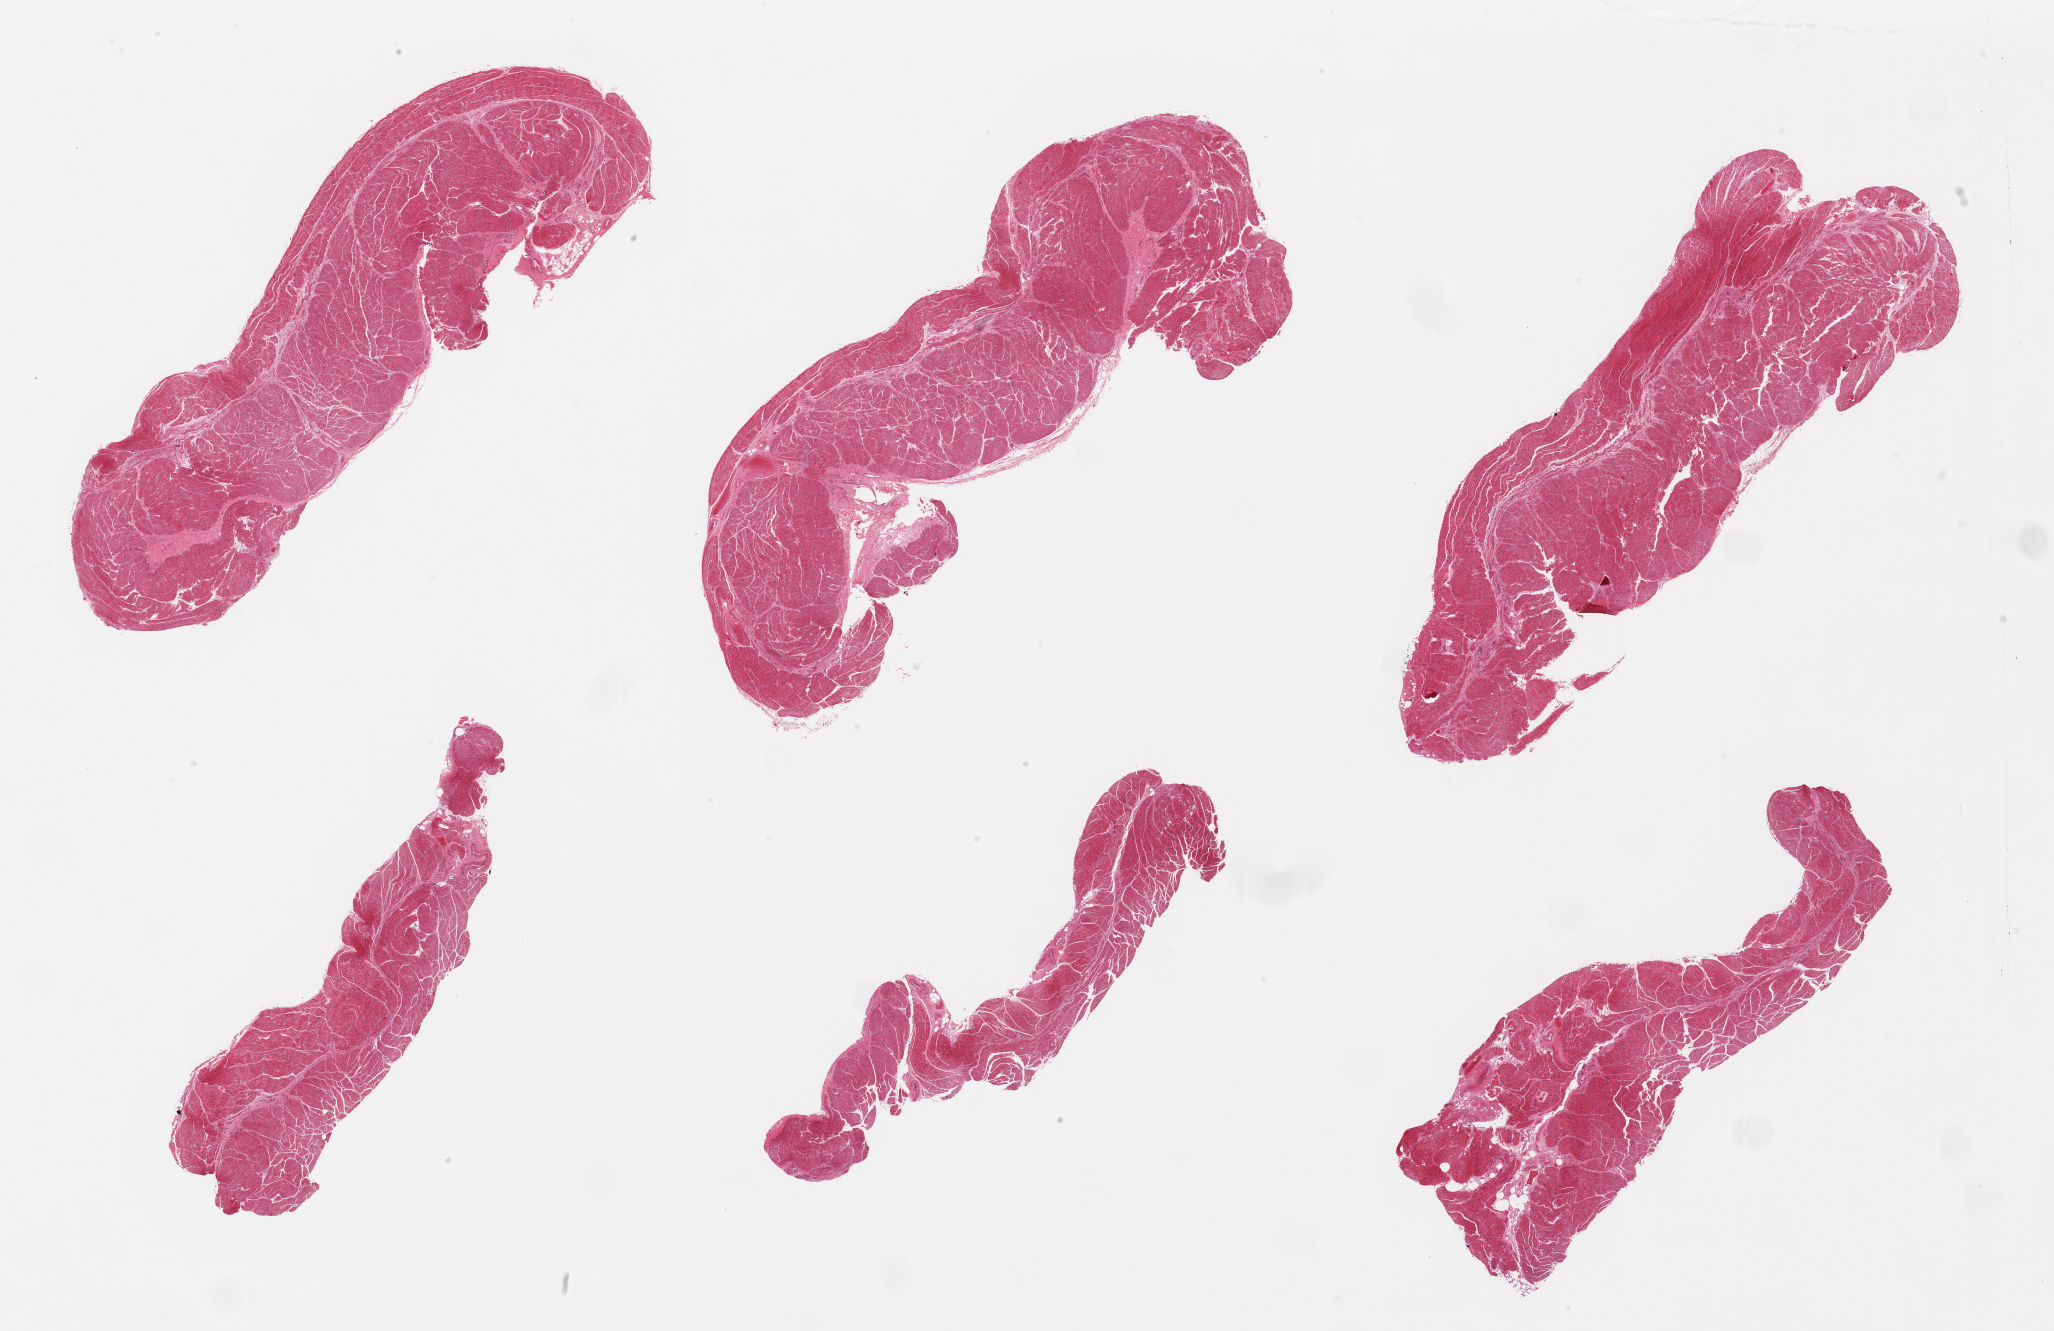
Digitized hematoxylin and eosin (H&E)-stained section, a low-resolution overview of the entire scanned area, about 32.5 x 21.1 mm (slide scanned at 20x), PAXgene-fixed paraffin-embedded (PFPE) section, sampled site (target tissue): esophageal muscle, donor tissue sample.
Reviewer comment on this tissue sample: 6 pieces, target muscularis, trace adherent fat.